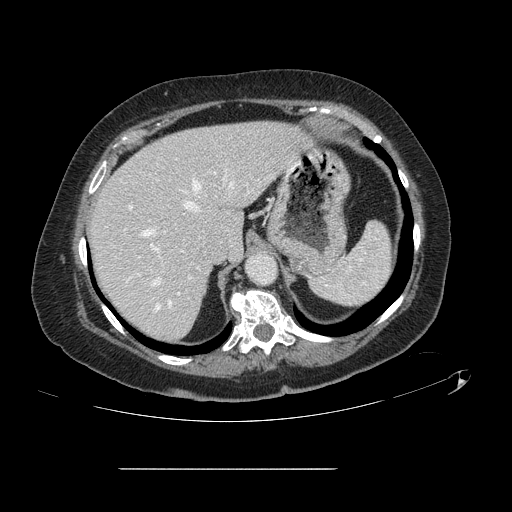
Contrast-enhanced abdominal CT, one axial slice. Slice 101 of 148 in the series (ordered by position). Intravenous contrast given. Soft-tissue window (W 400 / L 40 HU). 512 × 512 image matrix, field of view 439 × 439 mm. Female patient, age 75 years. Case-level facts recorded for this patient, not image findings: diagnosis: colorectal cancer liver metastases, imaged before liver resection; multiple liver metastases: no; largest metastasis: 2.4 cm; disease in both lobes: no.
Structures marked on this image (outlined manually by an expert reader):
- hepatic veins: bounding box [x1, y1, x2, y2] px = [141, 168, 235, 309]
- liver: [89, 122, 307, 341]
- planned liver remnant (the part of the liver to remain after resection): [90, 121, 307, 341]
- portal vein (with intrahepatic branches): [129, 180, 179, 294]